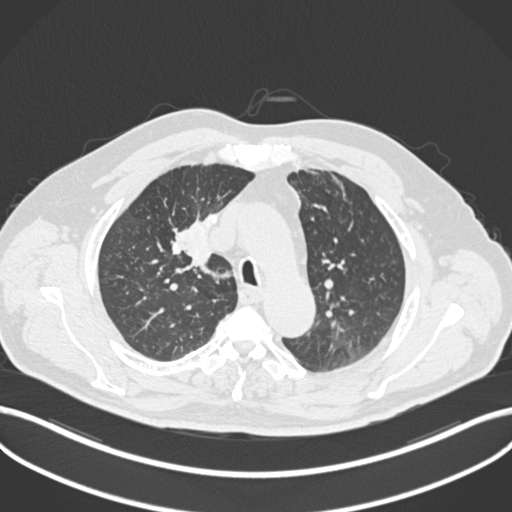
Chest CT, one axial slice; slice 146 of 255 in the series (ordered by position); reconstruction kernel B30f; lung window (W 1500 / L -600 HU); 1 mm slice thickness; 512 × 512 image matrix, field of view 400 × 400 mm. Patient: male, 60 years. From the clinical record (not read from this slice): clinical TNM (as recorded): T1b N1 M0.
Outlined on this slice (bounding box drawn by a radiologist):
- lung tumour (recorded histology: squamous cell carcinoma): bounding box (x1, y1, x2, y2) in pixels: (168, 214, 215, 277)